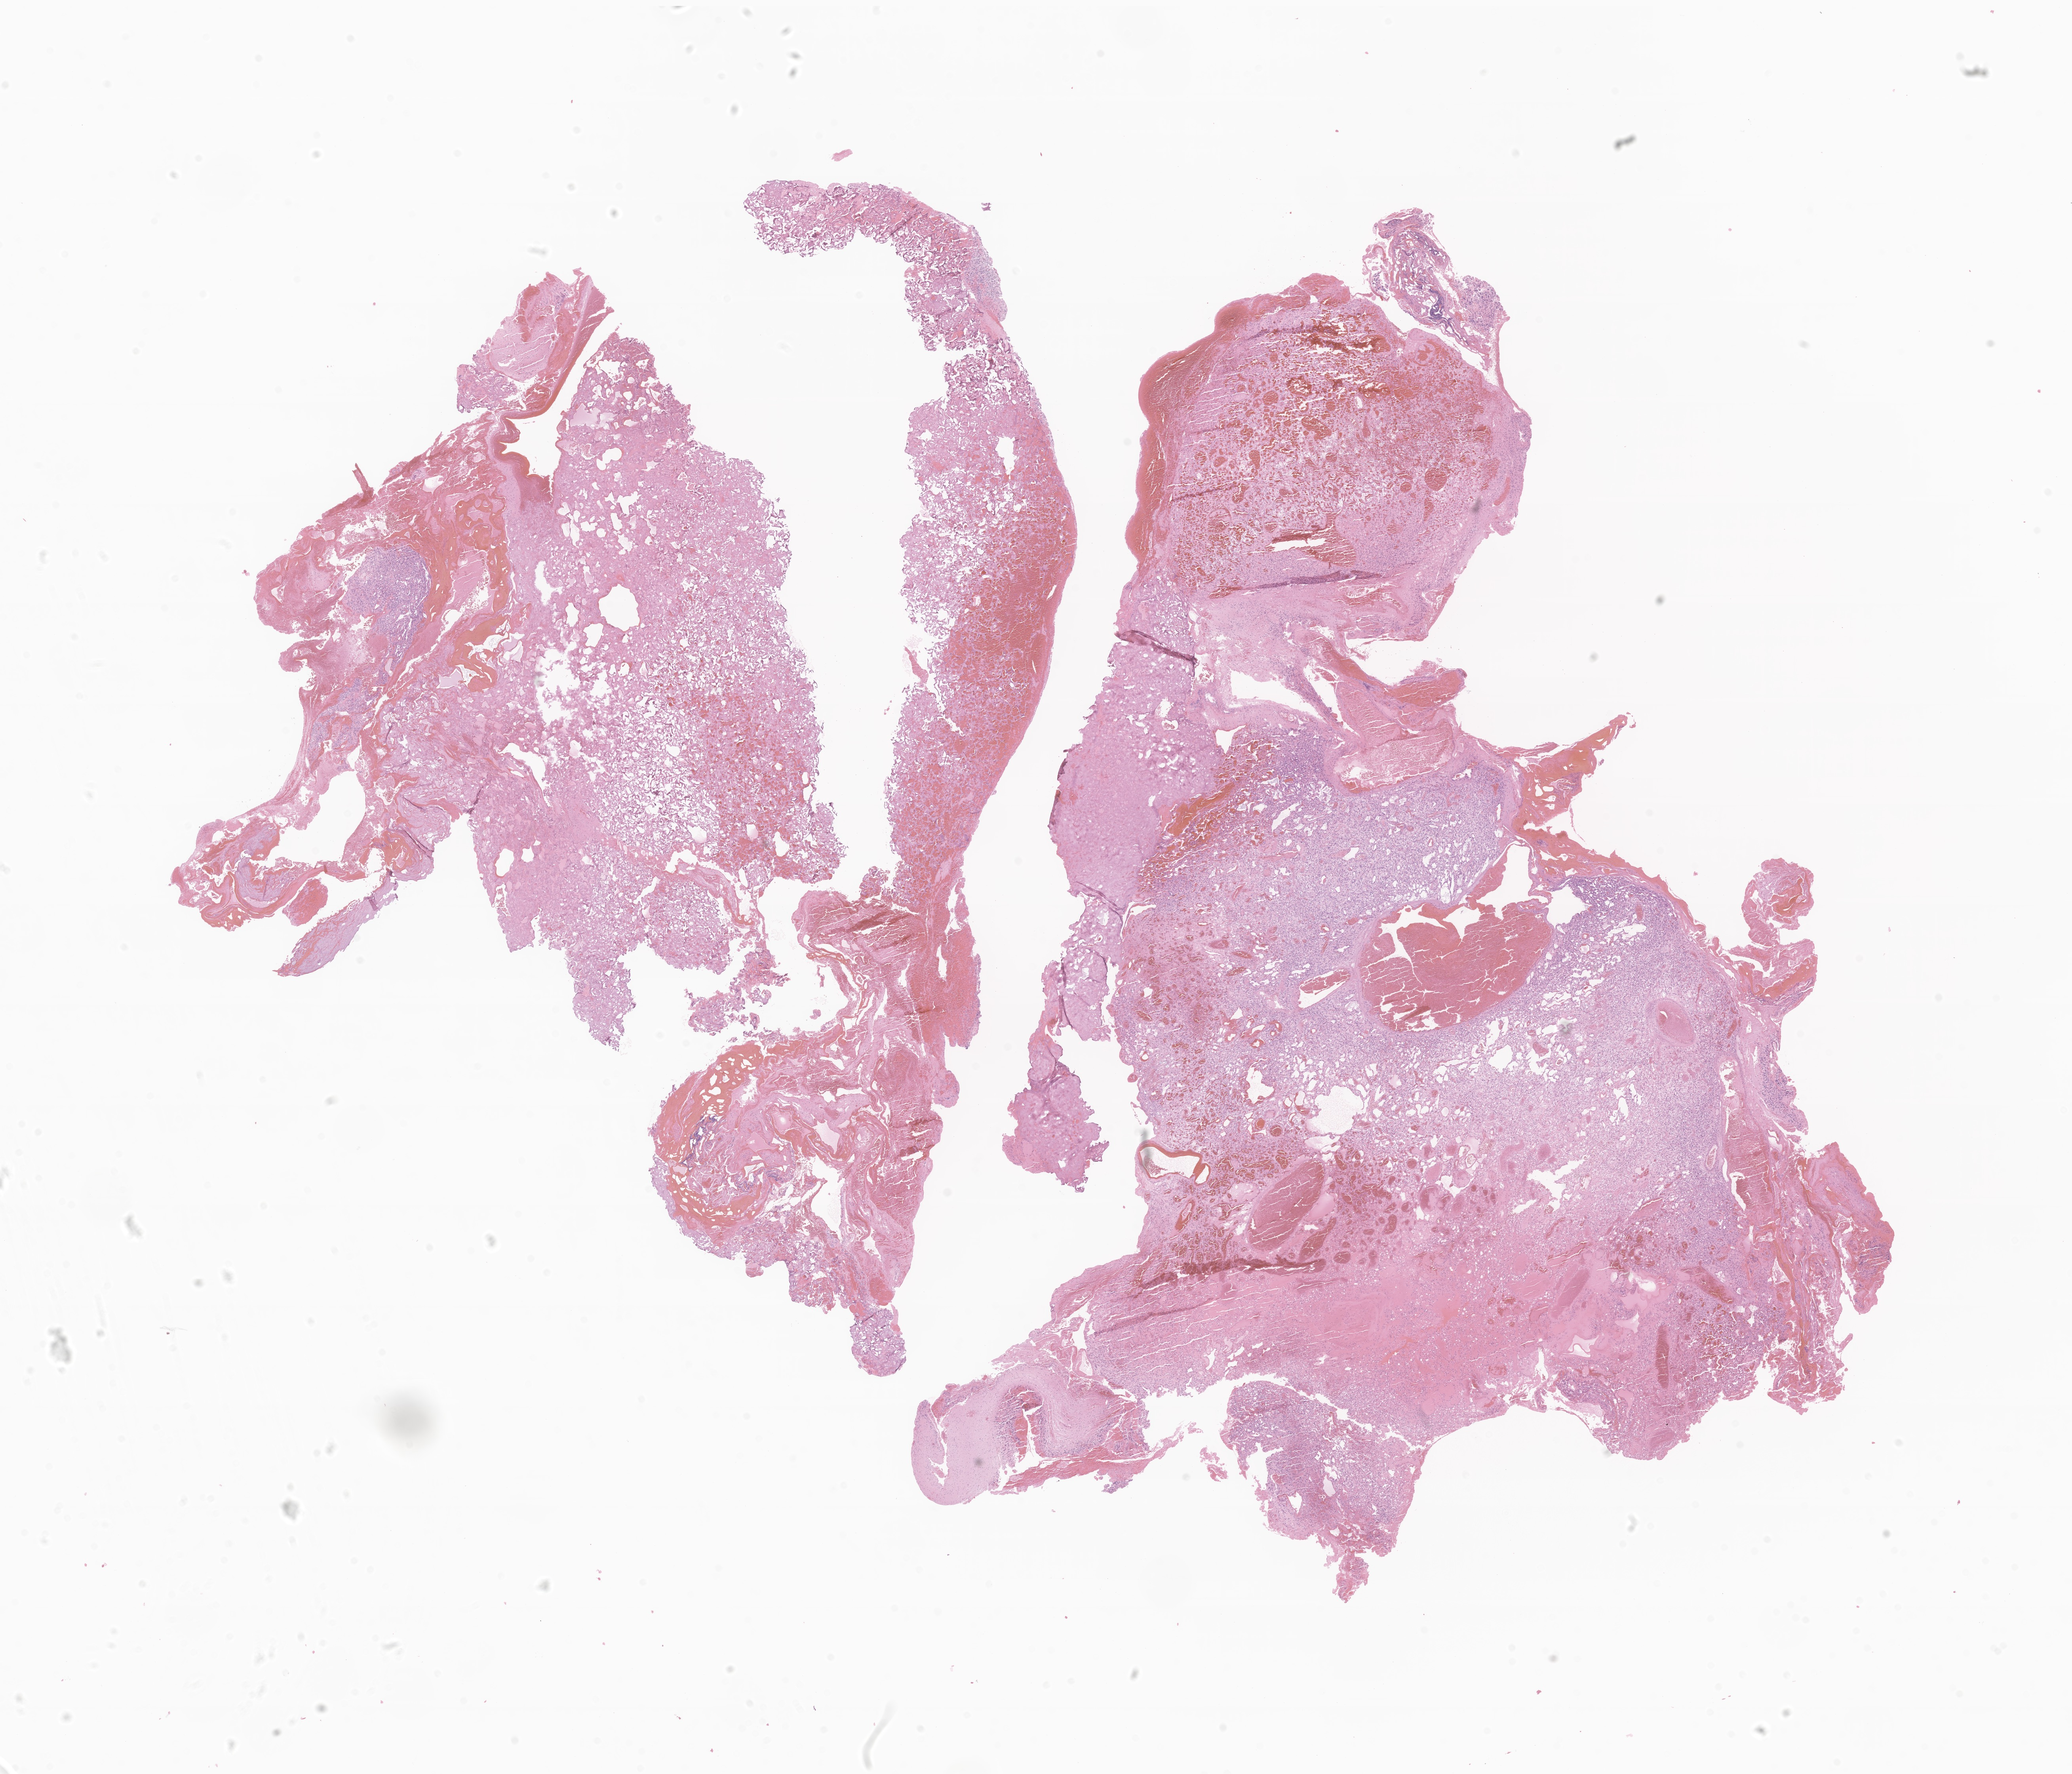
Haematoxylin and eosin whole-slide image of tumor tissue from the cerebellum, whole scanned area (about 22.1 x 18.9 mm) shown as a low-resolution overview, formalin-fixed, paraffin-embedded (FFPE) tissue. Male patient, age 221 months (18 years 5 months).
- diagnosis (ICD-O-3 morphology term): Hemangioblastoma